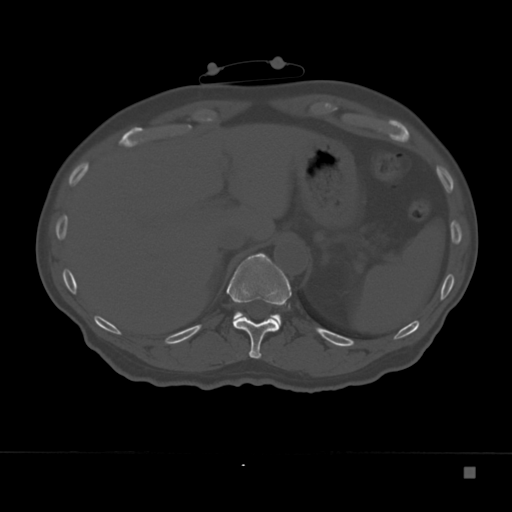
CT including the spine, one axial slice. Slice 148 of 332 in the series (ordered by position). Bone window (W 1800 / L 400 HU). 1.5 mm slice thickness. 512 × 512 image matrix, field of view 389 × 389 mm. Male patient, age 72 years. From the clinical record (not read from this slice): primary cancer: skeletal.
Outlined on this slice (semi-automatic segmentation, software-assisted and operator-edited):
- T11 vertebra: bounding box [x1, y1, x2, y2] px = [226, 253, 292, 359]
- T12 vertebra: [232, 311, 281, 328]